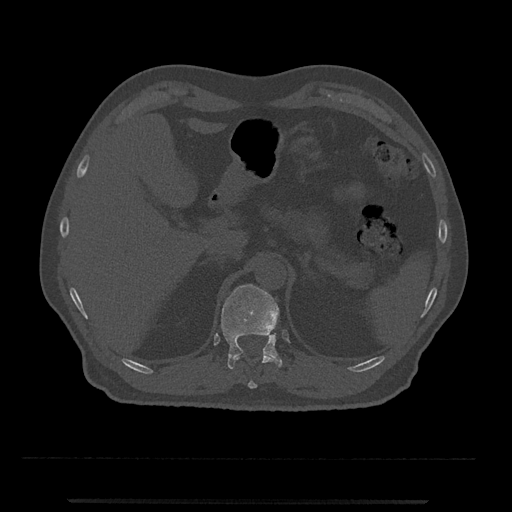
CT including the spine, one axial slice; slice 427 of 797 in the series (ordered by position); reconstruction kernel Br40s/3; 120 kVp; bone window (W 1800 / L 400 HU); 0.5 mm slice thickness; 512 × 512 image matrix, field of view 419 × 419 mm. Male patient, age 63 years. Case-level facts recorded for this patient, not image findings: primary cancer: prostate.
Outlined on this slice (semi-automatically segmented with operator editing):
- T11 vertebra: bounding box [x1, y1, x2, y2] px = [235, 352, 273, 389]
- T12 vertebra: [221, 284, 282, 369]